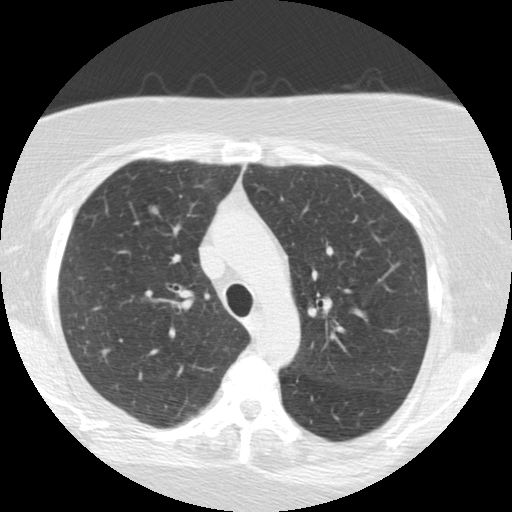
Low-dose screening chest CT, one axial slice; slice 167 of 225 in the series (ordered by position); reconstruction kernel STANDARD; lung window (W 1500 / L -600 HU); 2.5 mm slice thickness; 512 × 512 image matrix.
Structures marked on this image (manually delineated by an expert):
- lesion 1 (tumor, upper lobe of right lung): box from (x=151, y=207) to (x=158, y=214) px